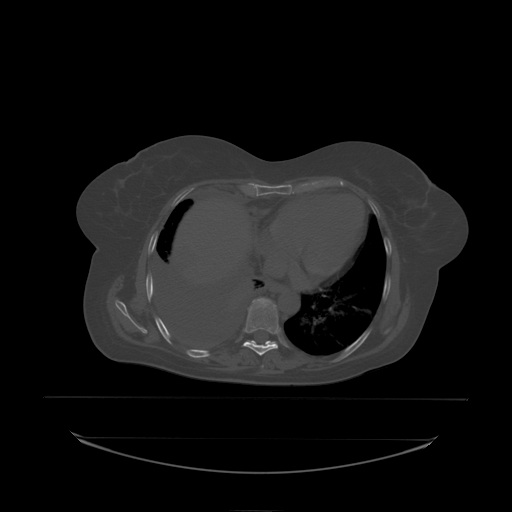
CT including the spine, one axial slice; slice 131 of 242 in the series (ordered by position); bone window (W 1800 / L 400 HU); 512 × 512 image matrix. Patient: female, 53 years. Case-level facts recorded for this patient, not image findings: primary cancer: lung.
Outlined on this slice (semi-automatically segmented with operator editing):
- T8 vertebra: bounding box <246,298,280,334> (left, top, right, bottom; pixels)